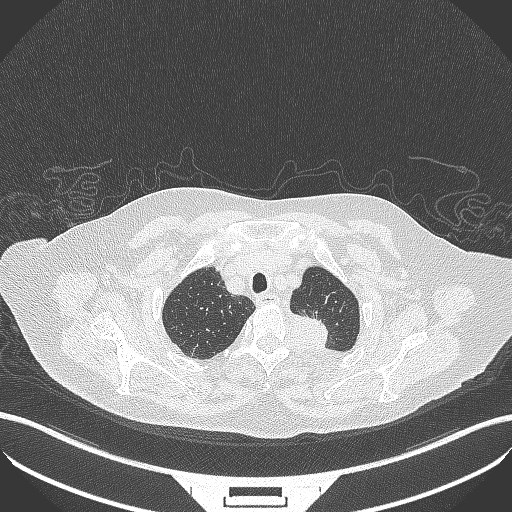
Chest CT, one axial slice; position 301 of 353 along the scan axis; 100 kVp; lung window (W 1500 / L -600 HU); 512 × 512 image matrix, field of view 400 × 400 mm. Patient: female, 81 years. From the clinical record (not read from this slice): clinical TNM (as recorded): T2a N0 M0.
Outlined on this slice (rectangle marked by the reading radiologist):
- lung tumour (recorded histology: adenocarcinoma): bounding box (x1, y1, x2, y2) in pixels: (286, 308, 332, 353)